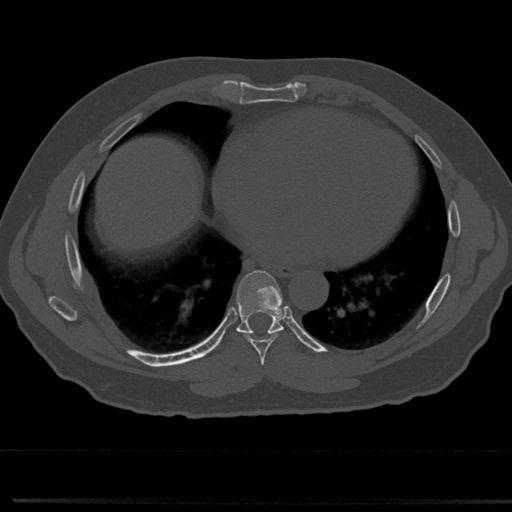
CT including the spine, one axial slice; slice 378 of 817 in the series (ordered by position); reconstruction kernel Br40s/3; bone window (W 1800 / L 400 HU); 512 × 512 image matrix, field of view 355 × 355 mm. Patient: male, 61 years. From the clinical record (not read from this slice): primary cancer: prostate.
Outlined on this slice (semi-automatic segmentation, software-assisted and operator-edited):
- T6 vertebra: bounding box [x1, y1, x2, y2] px = [261, 369, 266, 376]
- T7 vertebra: [232, 272, 292, 354]
- T8 vertebra: [242, 328, 247, 332]